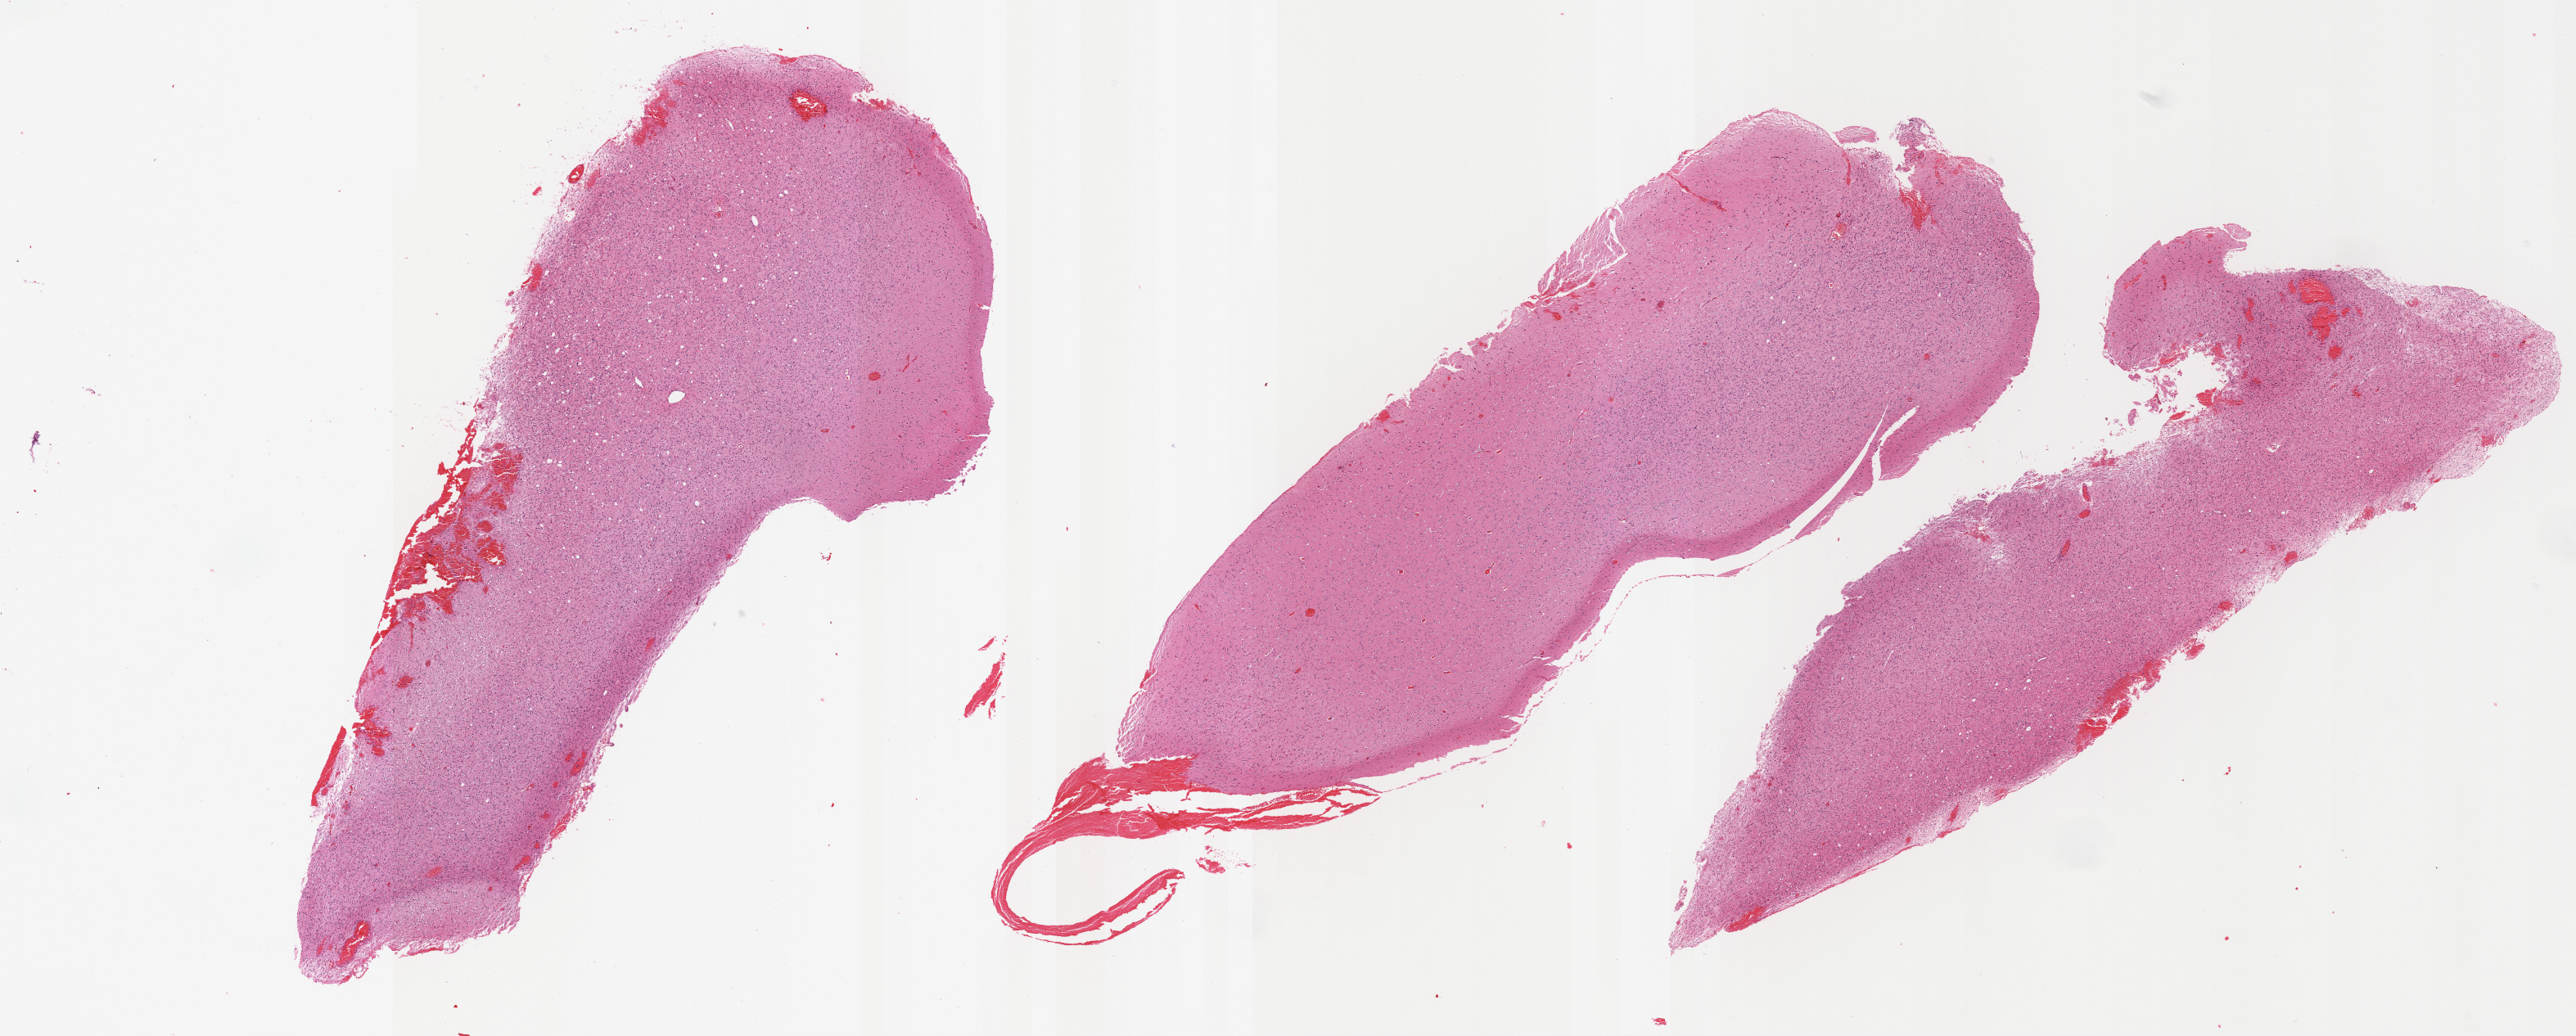
Hematoxylin and eosin (H&E) stained whole-slide image, a low-resolution overview of the entire scanned area, about 25.4 x 10.2 mm (acquisition: 40x scan), FFPE section, brain, primary tumour sample. Male patient; age at initial diagnosis 41 years.
Histologic diagnosis: Mixed glioma.